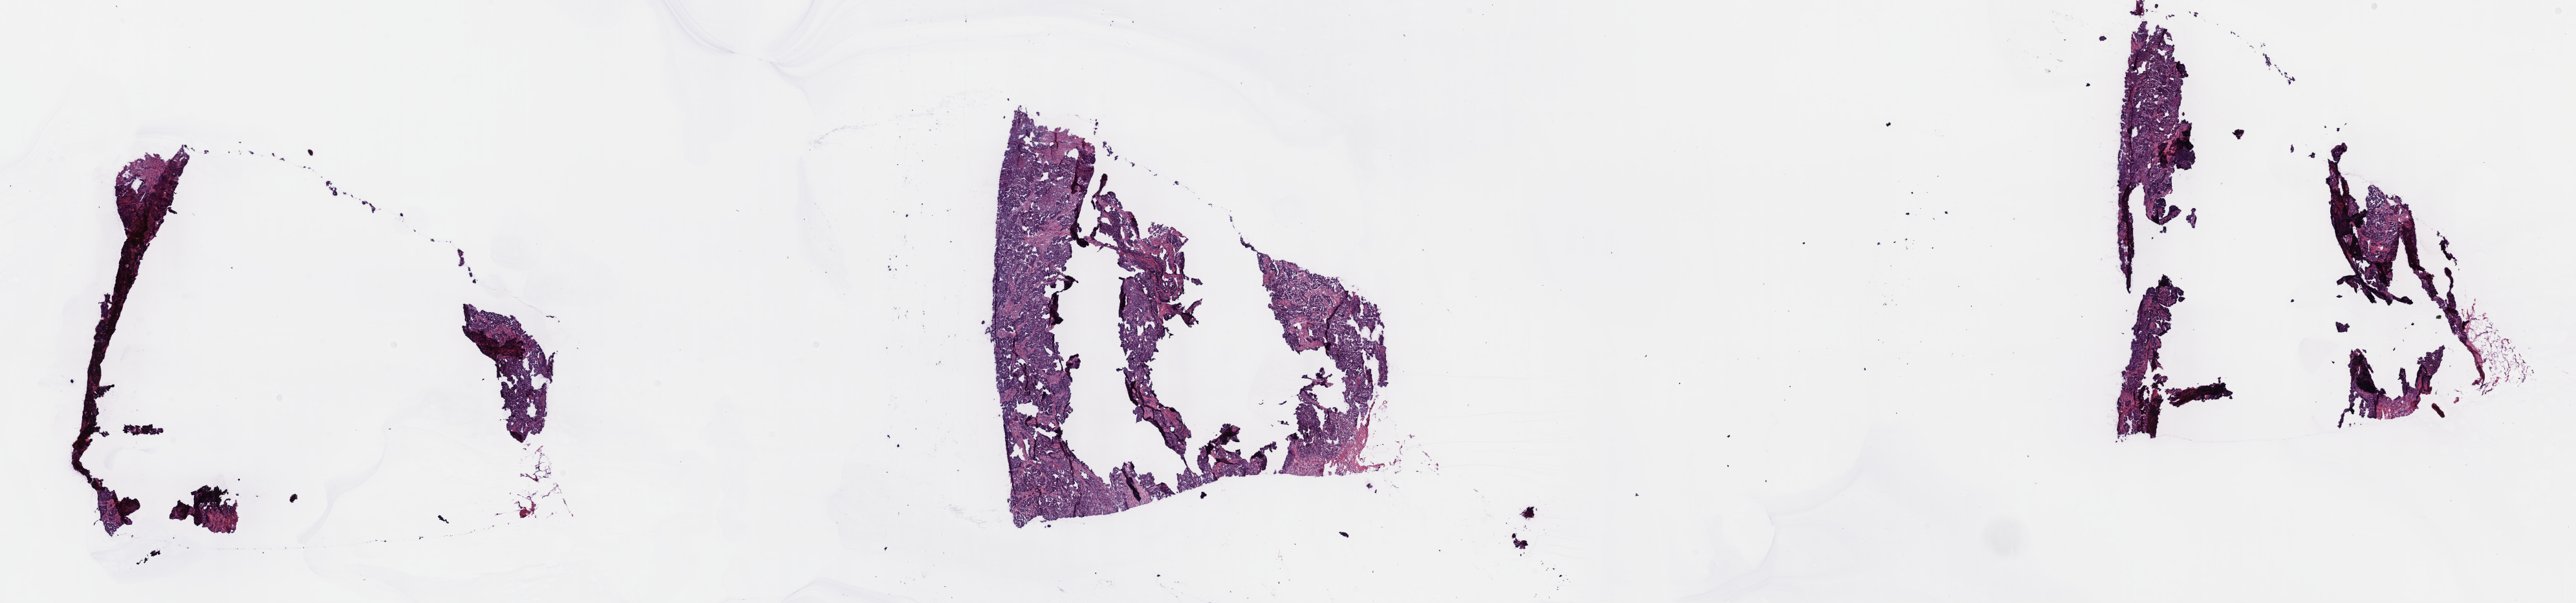
Hematoxylin and eosin (H&E) stained whole-slide image — shown as a low-resolution overview of the whole scanned area (about 32.2 x 7.5 mm, slide scanned at 40x). Frozen section. Mesothelium, primary tumour sample. Patient: male, age at initial diagnosis 67 years. Composition of this section per pathologist review: tumour cells 80%, tumour nuclei 80%, normal cells 0%, stromal cells 20%, necrosis 0%. Infiltration values recorded for this section: lymphocyte infiltration 4%, monocyte infiltration 1%, neutrophil infiltration 4%.
AJCC pathologic stage: II (7th edition). Diagnosis: Epithelioid mesothelioma, malignant (pleura, NOS). Laterality: right.